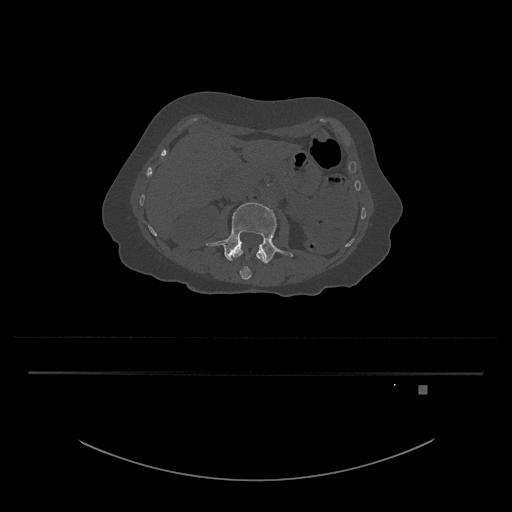
CT including the spine, one axial slice; slice 448 of 797 in the series (ordered by position); 120 kVp; bone window (W 1800 / L 400 HU); 0.5 mm slice thickness; 512 × 512 image matrix, field of view 500 × 500 mm. Patient: female, 57 years. From the clinical record (not read from this slice): primary cancer: cervical.
Structures marked on this image (semi-automatically segmented with operator editing):
- L3 vertebra: bounding box (x1, y1, x2, y2) in pixels: (206, 202, 293, 264)